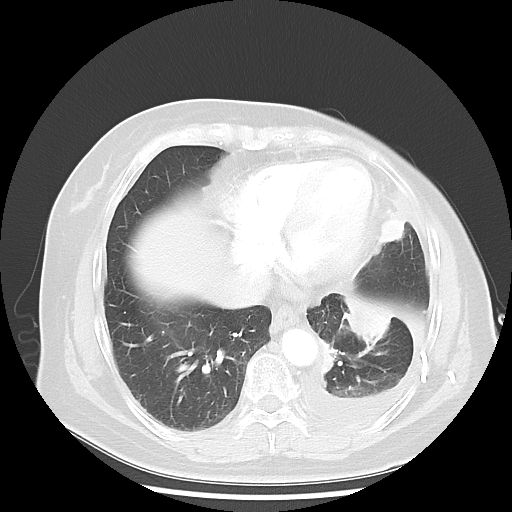
Chest CT, one axial slice; slice 14 of 48 in the series (ordered by position); reconstruction kernel LUNG; lung window (W 1500 / L -600 HU); 512 × 512 image matrix. Female patient, age 63 years. Case-level facts recorded for this patient, not image findings: clinical TNM (as recorded): T2 N0 M1.
Structures marked on this image (bounding box drawn by a radiologist):
- lung tumour (recorded histology: adenocarcinoma): box from (x=339, y=284) to (x=399, y=358) px